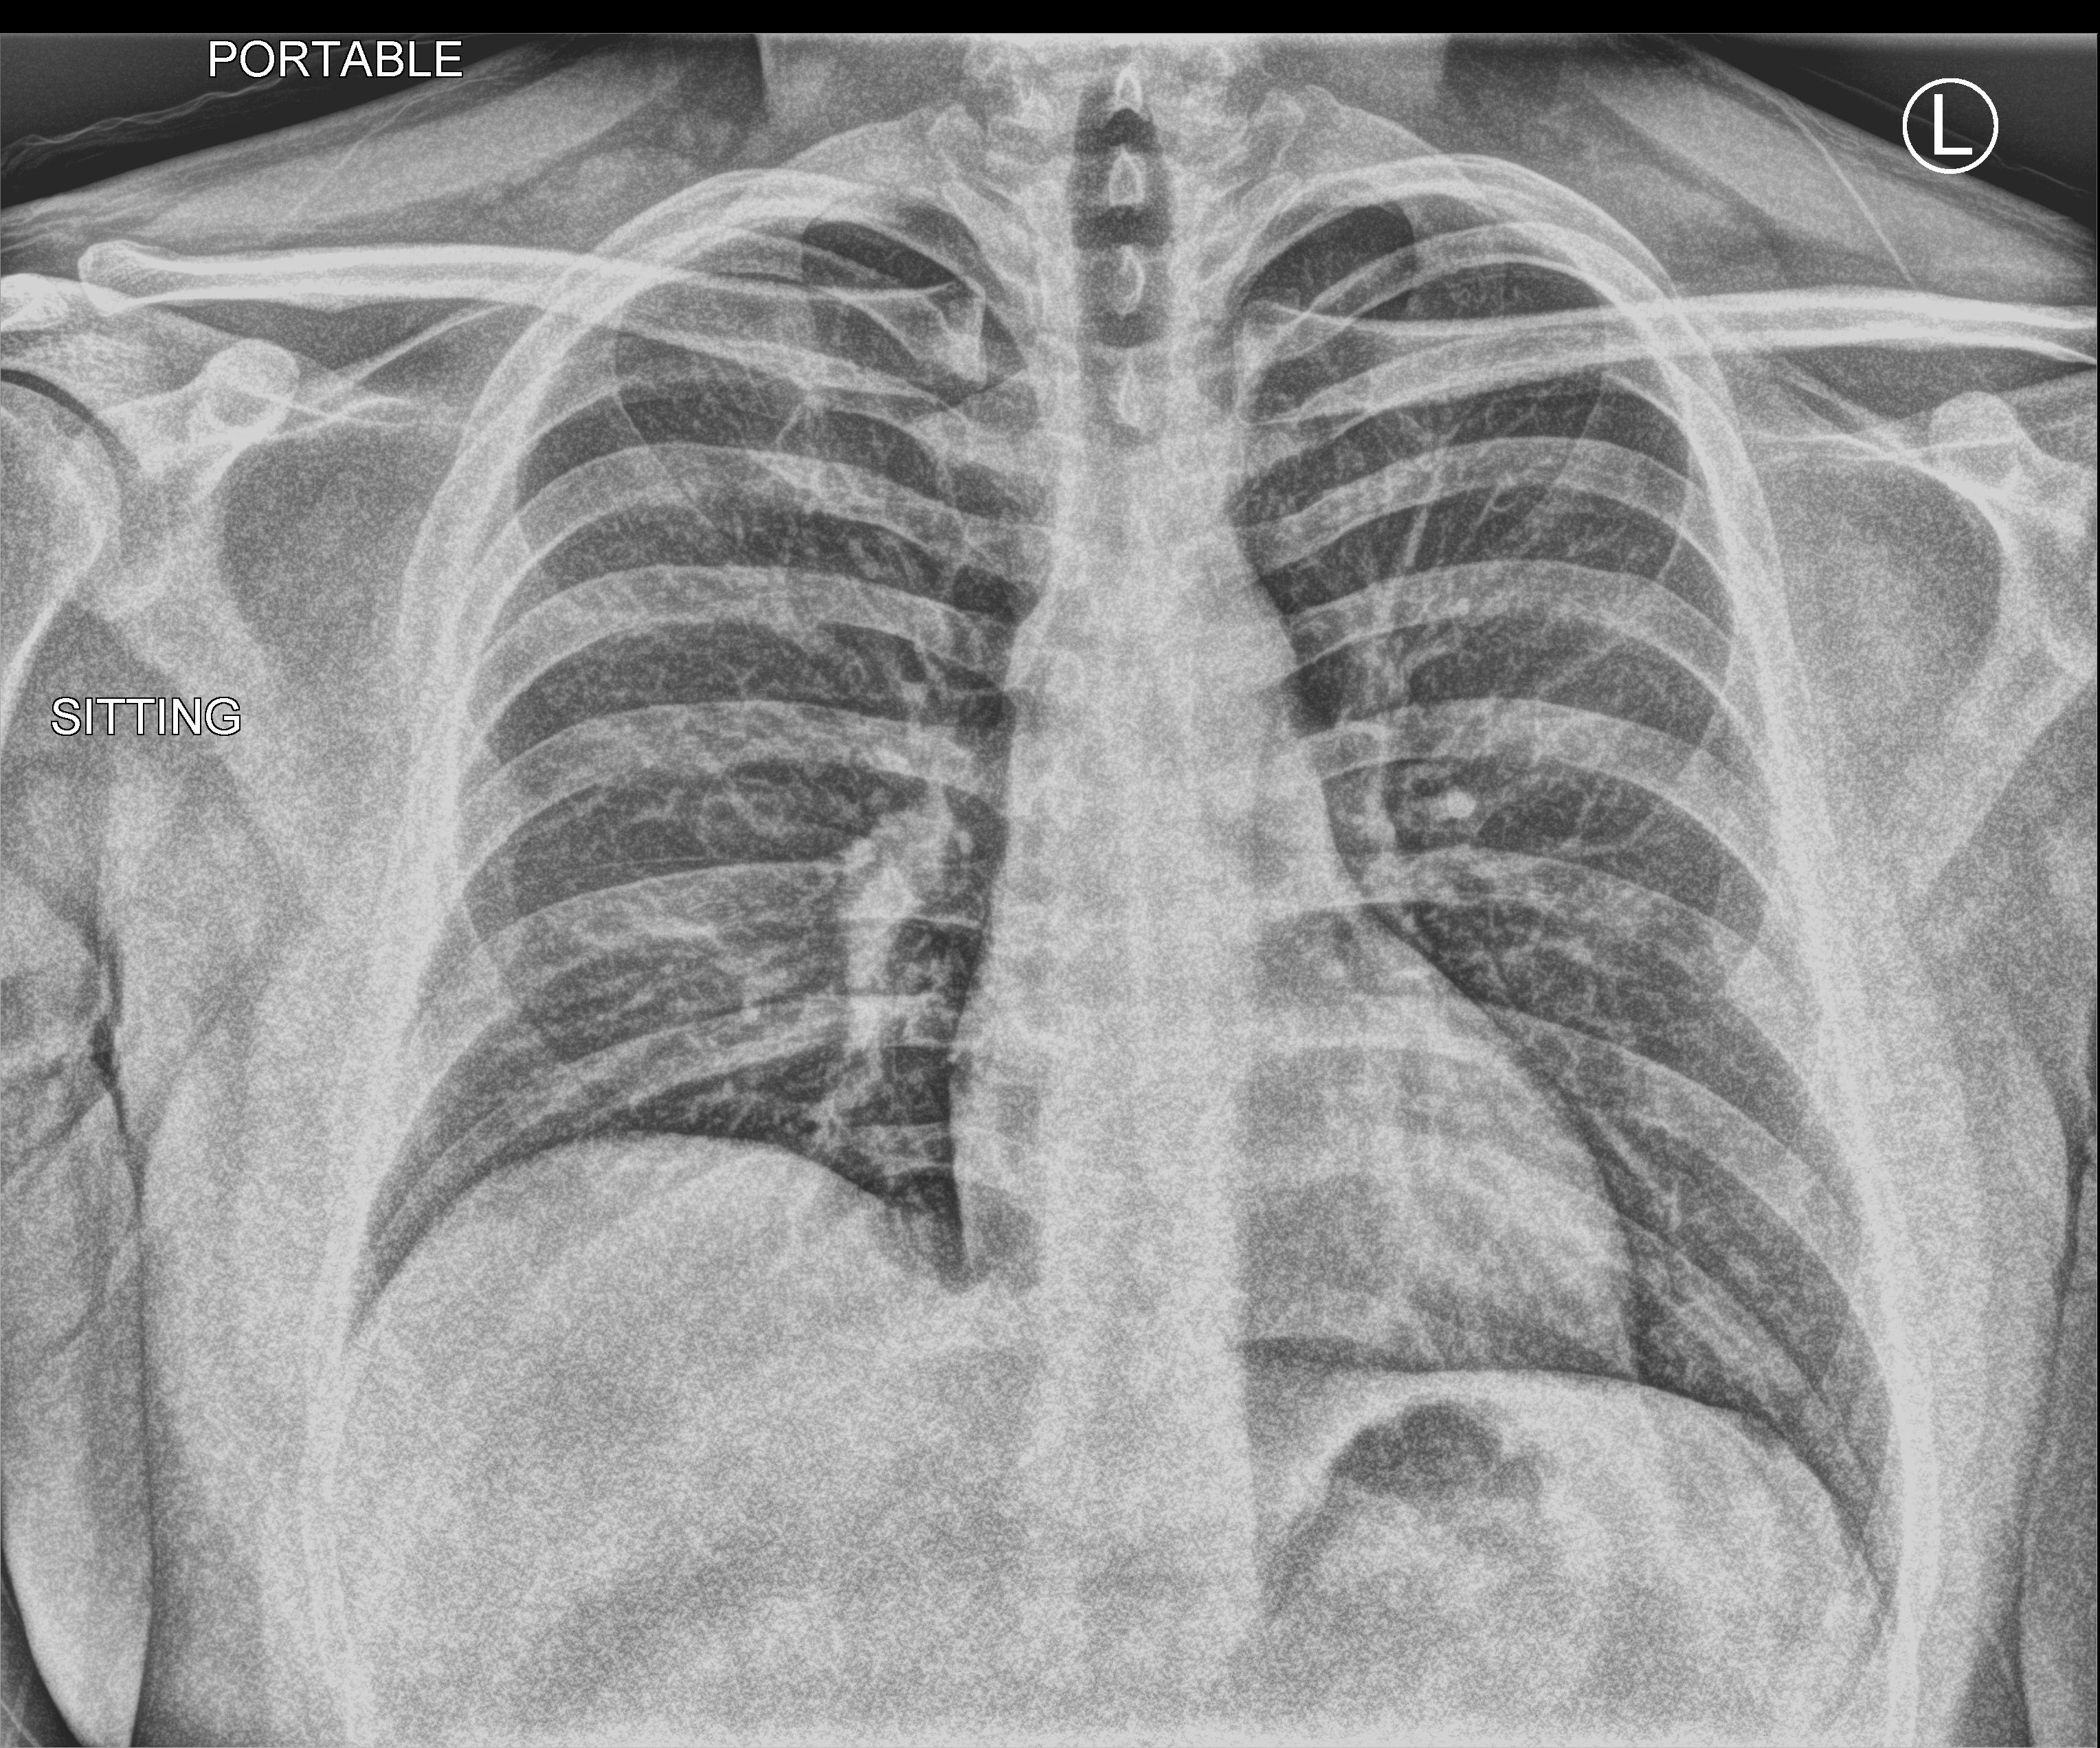
Bedside chest radiograph (computed radiography), anteroposterior (AP) projection. Patient hospitalised with COVID-19; male, aged 18–59 years.
Admission-level facts for this patient (not findings on this image; timing relative to this image not recorded): hypertension (admission record): no.